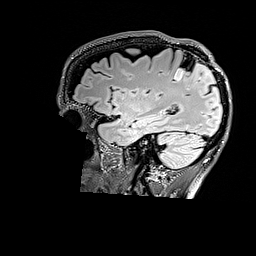
Brain MRI from a brain-tumour surgery series, one sagittal slice. Slice 121 of 176 in the series (ordered by position). T2 FLAIR. 1 mm slice thickness. 256 × 256 image matrix, field of view 256 × 256 mm. Case-level facts recorded for this patient, not image findings: histopathology: Astrocytoma; WHO grade: 3; IDH mutation: yes.
Structures marked on this image (outlined manually by an expert reader):
- tumour: bounding box <174,63,211,80> (left, top, right, bottom; pixels)
- tumour: <206,77,211,80>